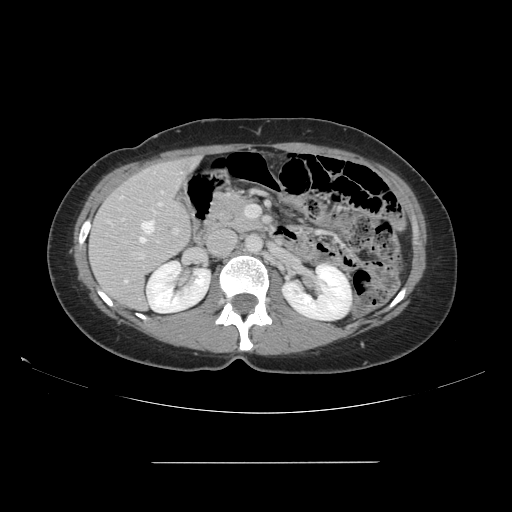
Contrast-enhanced abdominal CT, one axial slice. Position 77 of 151 along the scan axis. 120 kVp. Intravenous contrast given. Soft-tissue window (W 400 / L 40 HU). 512 × 512 image matrix, field of view 421 × 421 mm. Female patient, age 46 years. Case-level facts recorded for this patient, not image findings: diagnosis: colorectal cancer liver metastases, imaged before liver resection; multiple liver metastases: yes; largest metastasis: 3 cm; disease in both lobes: yes.
Outlined on this slice (manually delineated by an expert):
- hepatic veins: bounding box [x1, y1, x2, y2] px = [121, 196, 155, 243]
- liver: [90, 158, 197, 310]
- planned liver remnant (the part of the liver to remain after resection): [94, 158, 197, 310]
- portal vein (with intrahepatic branches): [123, 190, 246, 260]